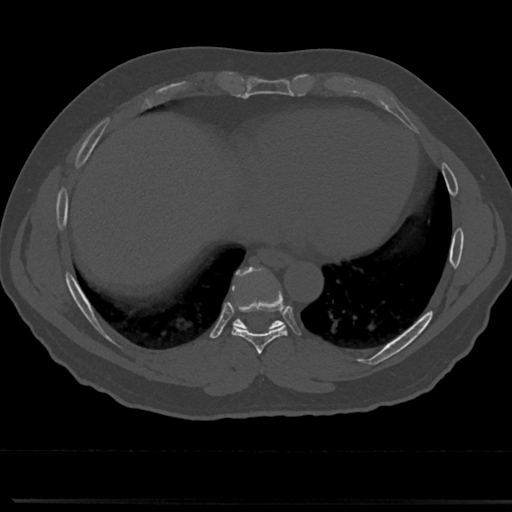
CT including the spine, one axial slice. Slice 340 of 817 in the series (ordered by position). 120 kVp. Bone window (W 1800 / L 400 HU). 512 × 512 image matrix. Male patient, age 61 years. Case-level facts recorded for this patient, not image findings: primary cancer: prostate.
Outlined on this slice (semi-automatic segmentation, software-assisted and operator-edited):
- T7 vertebra: bounding box <257,343,268,377> (left, top, right, bottom; pixels)
- T8 vertebra: <214,271,308,355>